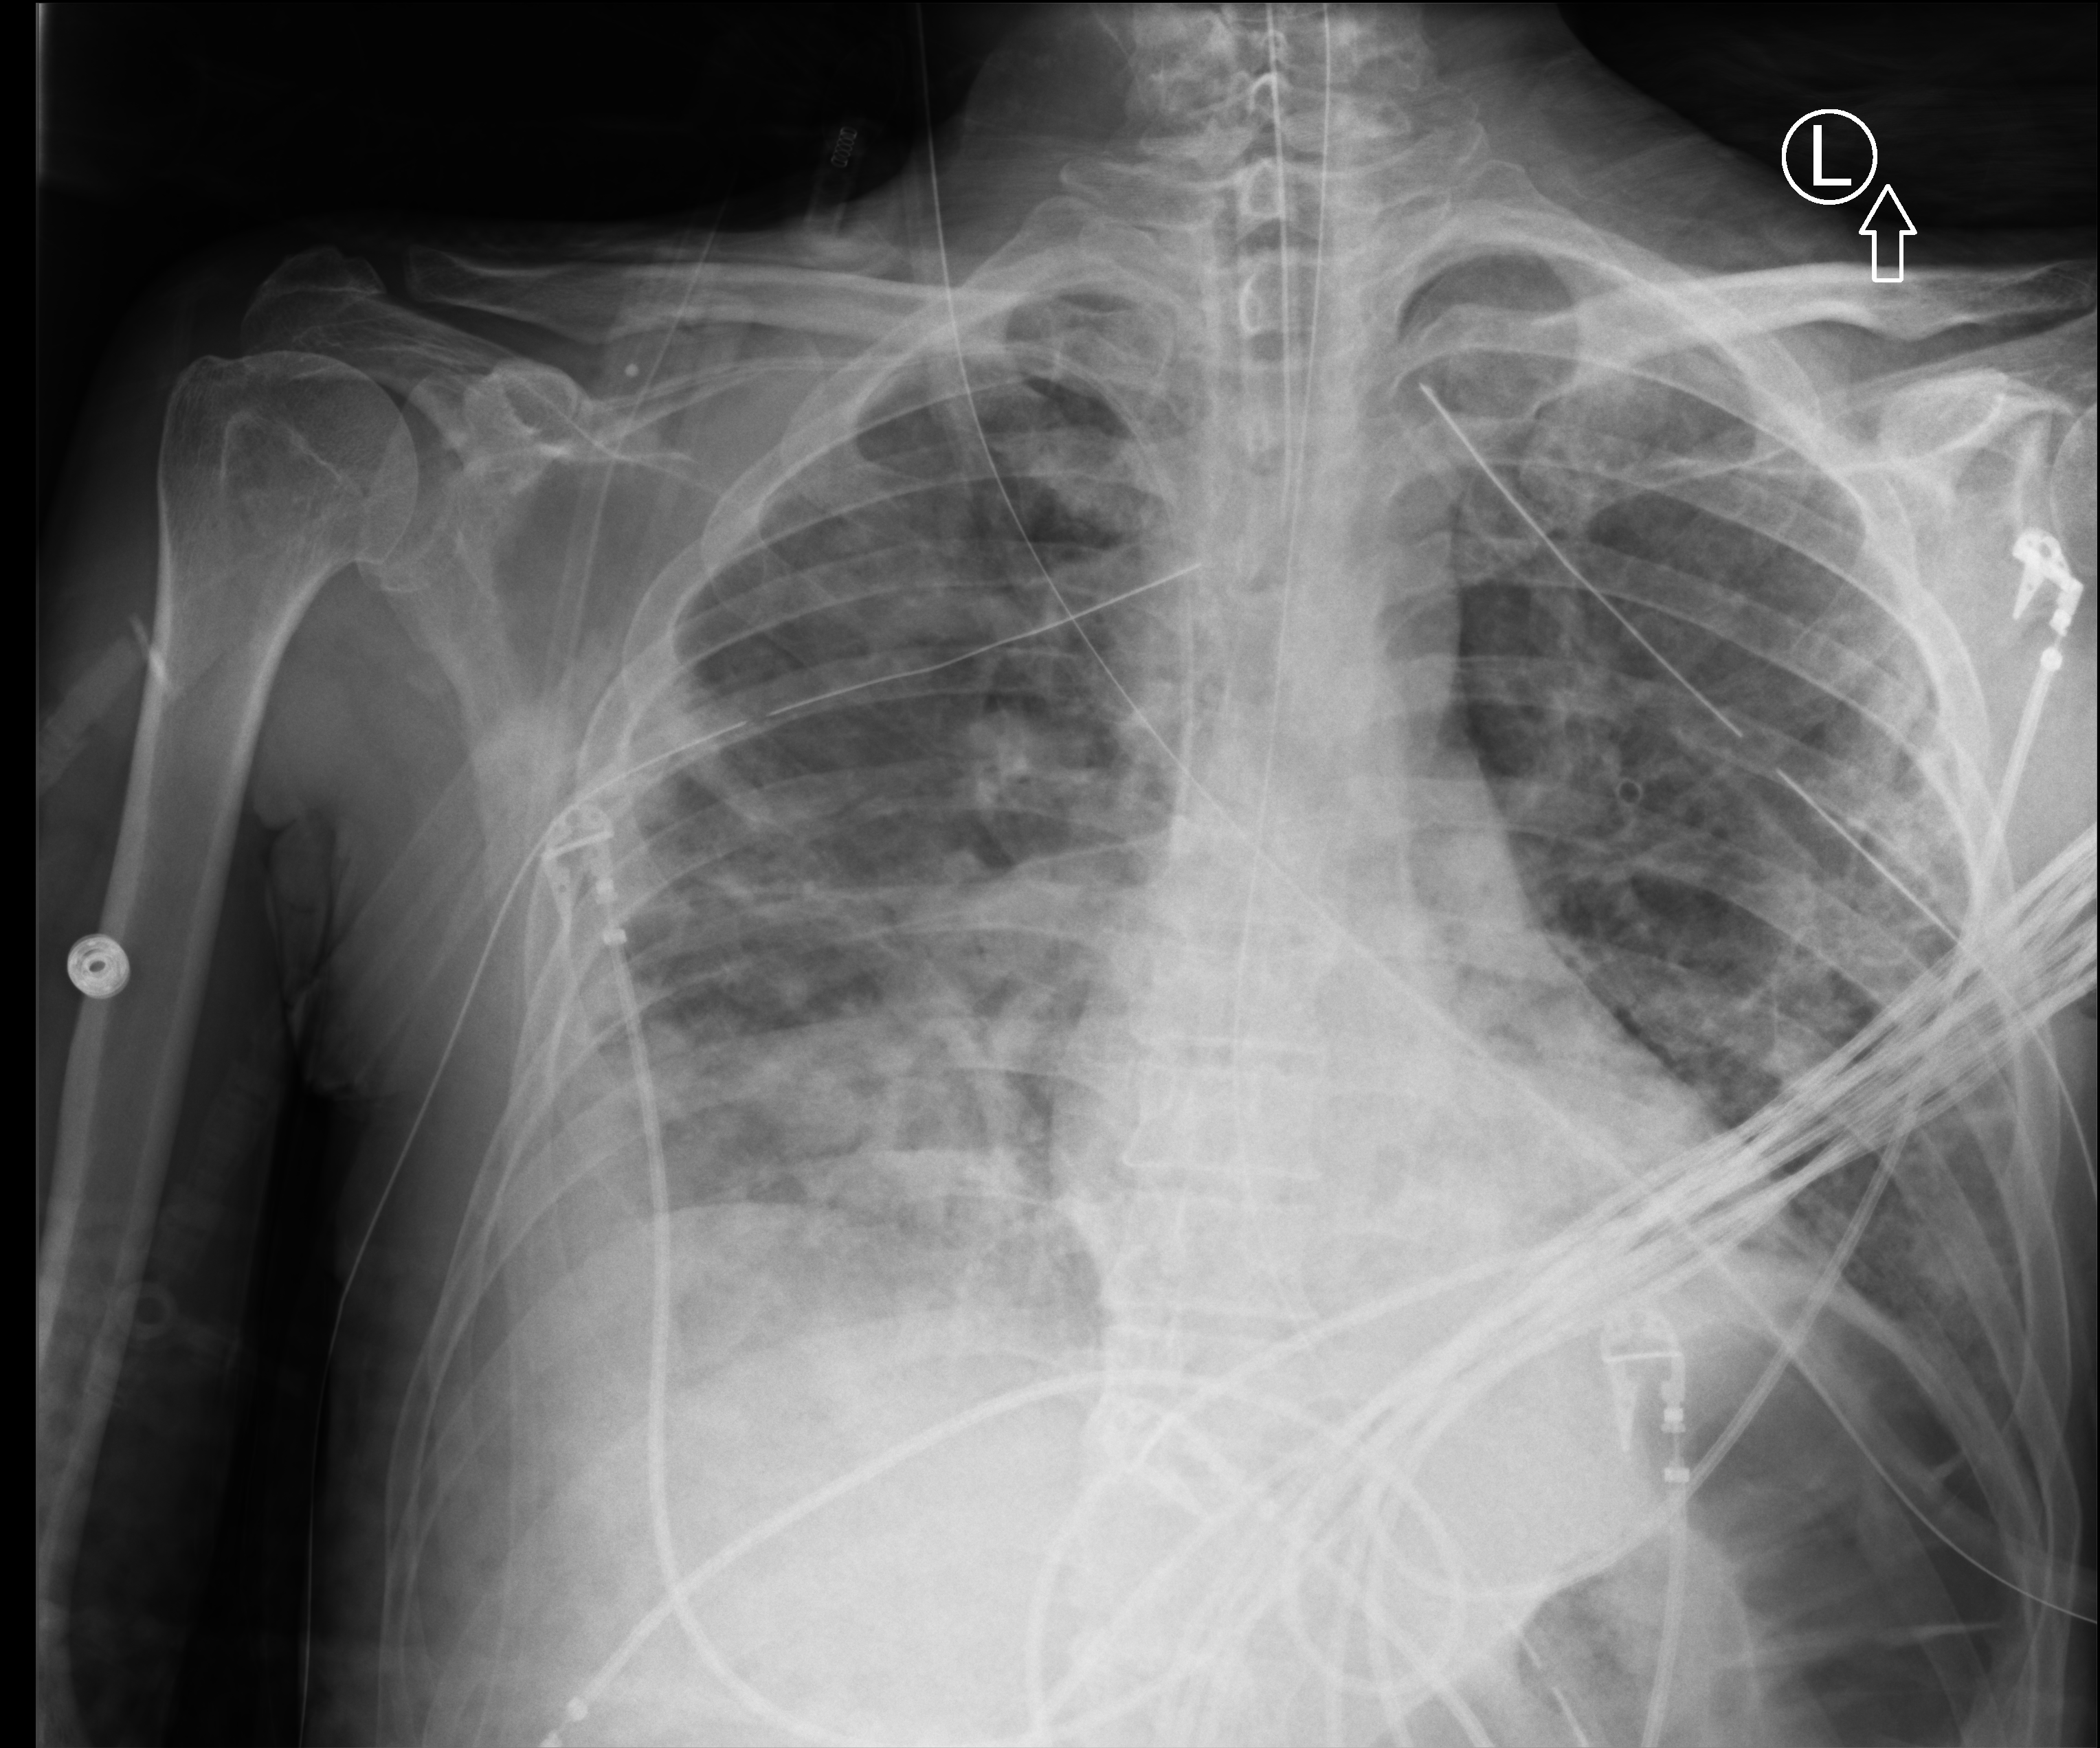
Bedside chest radiograph (computed radiography); anteroposterior (AP) projection. Male patient hospitalised with COVID-19, age 18–59 years.
Hospital-stay facts (about this admission, not read from this image; timing relative to this image not recorded): diabetes (admission record): yes; length of hospital stay: 96 days.